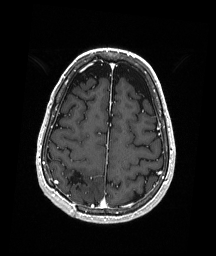
Brain MRI from a brain-tumour surgery series, one axial slice. Slice 62 of 192 in the series (ordered by position). T1-weighted post-contrast. 1 mm slice thickness. 216 × 256 image matrix. From the clinical record (not read from this slice): histopathology: Astrocytoma; WHO grade: 3; IDH mutation: yes.
Outlined on this slice (expert manual segmentation):
- previous resection cavity: box from (x=67, y=171) to (x=87, y=194) px